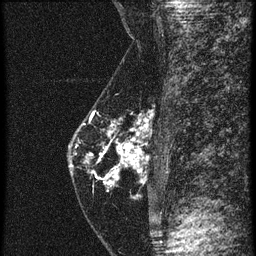
Breast MRI (dynamic contrast-enhanced), one sagittal slice. Slice 21 of 60 in the series (ordered by position). 4 images stored at this slice position (order not interpretable as contrast timing). 1.5 T. TE 4.2 ms, TR 20.4 ms. 1.5 mm slice thickness. 256 × 256 image matrix, field of view 180 × 180 mm. Patient: female, 46 years. From the clinical record (not read from this slice): setting: breast cancer imaged before/during neoadjuvant chemotherapy; receptor status: triple-negative.
Annotated regions visible in this slice (semi-automatic segmentation, software-assisted and operator-edited):
- analysis volume of interest (the breast-tissue region the enhancement analysis was run in; not a lesion): bounding box (x1, y1, x2, y2) in pixels: (68, 82, 145, 201)
- tumour enhancement mask (voxels above the 90 % enhancement threshold inside the analysis volume of interest): (88, 130, 142, 185)